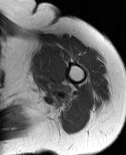
MRI of an extremity soft-tissue mass, one axial slice. Slice 63 of 86 in the series (ordered by position). MR volume resampled by the dataset authors to the PET/CT grid (not the native acquisition matrix). 3.27 mm slice thickness. 126 × 155 image matrix. Female patient. From the clinical record (not read from this slice): histological type: pleiomorphic leiomyosarcoma; grade: high; site of the primary tumour: left biceps.
Outlined on this slice (expert contour drawn on MRI and transferred to this co-registered scan by the dataset authors):
- gross tumour volume including surrounding oedema: bounding box [x1, y1, x2, y2] px = [29, 47, 60, 96]
- gross tumour volume (mass): [31, 51, 57, 77]